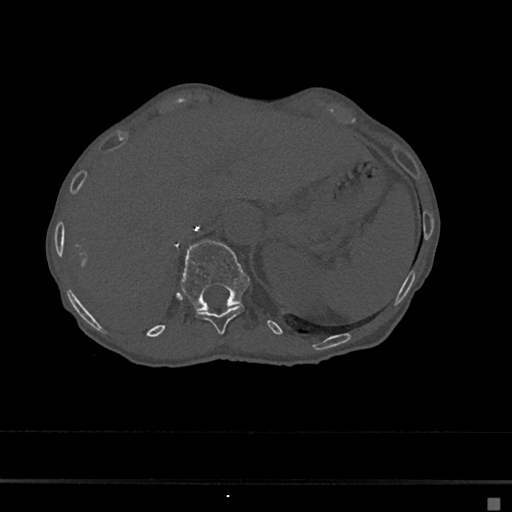
CT including the spine, one axial slice; position 147 of 797 along the scan axis; reconstruction kernel Br40s/3; 120 kVp; bone window (W 1800 / L 400 HU); 0.5 mm slice thickness; 512 × 512 image matrix, field of view 360 × 360 mm. Female patient, age 68 years. From the clinical record (not read from this slice): primary cancer: renal.
Annotated regions visible in this slice (semi-automatically segmented with operator editing):
- T11 vertebra: box from (x=195, y=304) to (x=244, y=335) px
- T12 vertebra: (x=181, y=240)–(x=250, y=311)